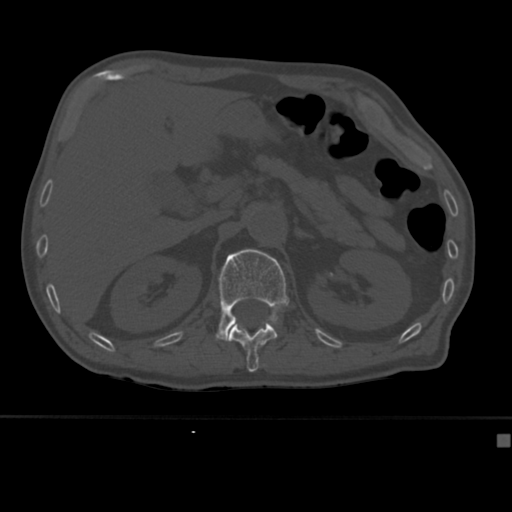
CT including the spine, one axial slice. Position 178 of 430 along the scan axis. 120 kVp. Bone window (W 1800 / L 400 HU). 512 × 512 image matrix. Patient: male, 64 years. From the clinical record (not read from this slice): primary cancer: uterus; vertebrae with lytic lesions (as recorded): T1, T4, T5, T7, L5.
Outlined on this slice (semi-automatically segmented with operator editing):
- L1 vertebra: box from (x=215, y=249) to (x=289, y=342) px
- T12 vertebra: (x=229, y=319)–(x=278, y=372)